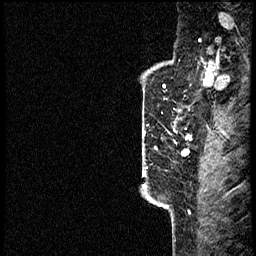
Breast MRI (dynamic contrast-enhanced), one sagittal slice. Position 52 of 60 along the scan axis. Dynamic contrast-enhanced study with each time point stored as its own series, time point 2 of 4 at this slice position (early post-contrast, ordered by acquisition time). 1.5 T. TE 4.2 ms, TR 17.6 ms. 2 mm slice thickness. 256 × 256 image matrix, field of view 200 × 200 mm. Female patient, age 40 years. Case-level facts recorded for this patient, not image findings: setting: breast cancer imaged before/during neoadjuvant chemotherapy; receptor status: HER2-positive.
Structures marked on this image (semi-automatic segmentation, software-assisted and operator-edited):
- analysis volume of interest (the breast-tissue region the enhancement analysis was run in; not a lesion): bounding box (x1, y1, x2, y2) in pixels: (142, 56, 197, 205)
- tumour enhancement mask (voxels above the 100 % enhancement threshold inside the analysis volume of interest): (142, 118, 191, 169)